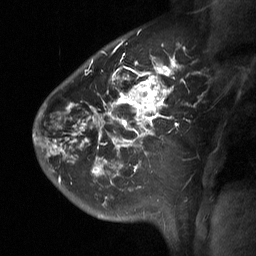
Breast MRI (dynamic contrast-enhanced), one sagittal slice; position 47 of 64 along the scan axis; dynamic contrast-enhanced study with each time point stored as its own series, time point 2 of 3 at this slice position (early post-contrast, ordered by acquisition time); 1.5 T; TE 4.8 ms, TR 27 ms; 256 × 256 image matrix, field of view 200 × 200 mm. Patient: female, 42 years. Case-level facts recorded for this patient, not image findings: setting: breast cancer imaged before/during neoadjuvant chemotherapy; receptor status: triple-negative.
Annotated regions visible in this slice (semi-automatically segmented with operator editing):
- analysis volume of interest (the breast-tissue region the enhancement analysis was run in; not a lesion): bounding box (x1, y1, x2, y2) in pixels: (49, 45, 199, 197)
- tumour enhancement mask (voxels above the 90 % enhancement threshold inside the analysis volume of interest): (50, 58, 179, 175)